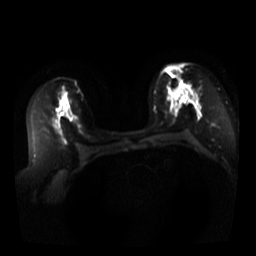
Breast MRI, one axial slice. Position 21 of 44 along the scan axis. Diffusion-weighted series; image 2 of 4 stored at this slice position (different b-values; order by instance number). 3 T. 256 × 256 image matrix, field of view 340 × 340 mm. Female patient.
Outlined on this slice (expert manual segmentation):
- tumour on diffusion-weighted imaging: bounding box (x1, y1, x2, y2) in pixels: (166, 65, 188, 91)